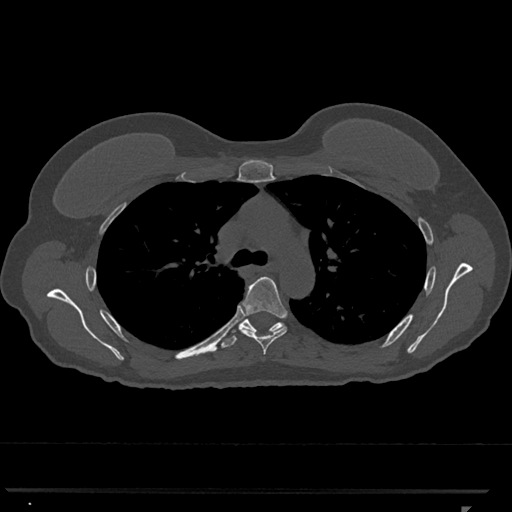
CT including the spine, one axial slice; position 792 of 793 along the scan axis; reconstruction kernel Br40s/3; 120 kVp; bone window (W 1800 / L 400 HU); 0.5 mm slice thickness; 512 × 512 image matrix. Patient: female, 62 years. Case-level facts recorded for this patient, not image findings: primary cancer: renal.
Structures marked on this image (semi-automatically segmented with operator editing):
- T5 vertebra: bounding box [x1, y1, x2, y2] px = [239, 277, 288, 355]
- T6 vertebra: [221, 315, 283, 349]